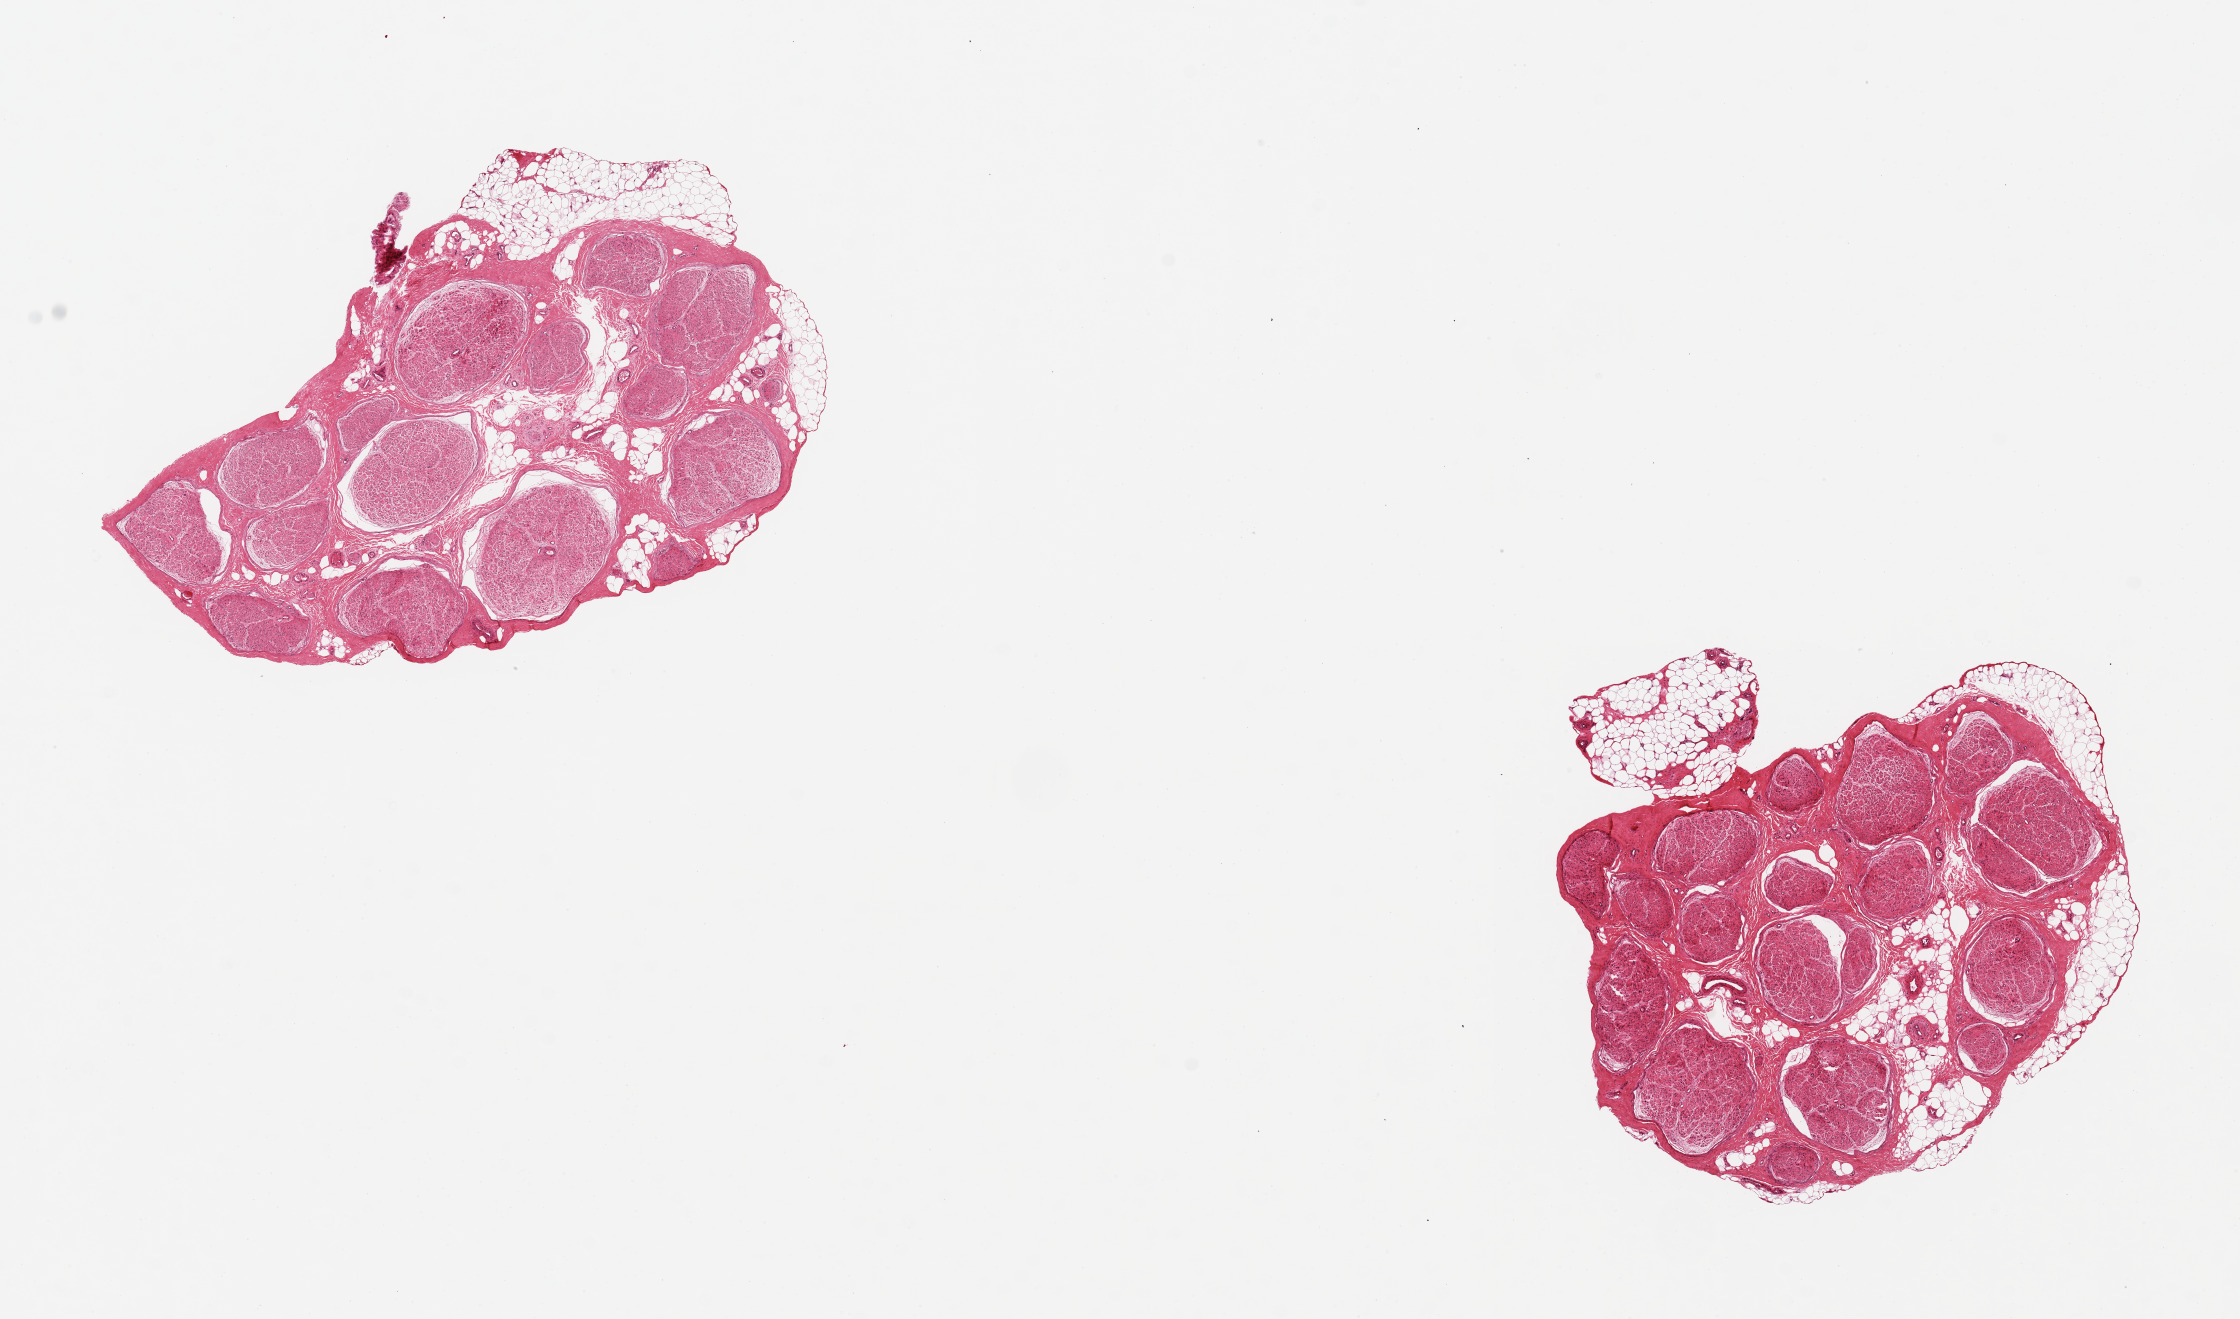
H&E whole-slide image, shown as a low-resolution overview of the whole scanned area (about 17.7 x 10.4 mm), PAXgene-fixed, paraffin-embedded tissue, target tissue: tibial nerve, tissue donor sample. Donor sex: male.
Reviewer comment on this tissue sample: 2 pieces ~5mm d. Minimal (`0.5mm) discontinuous foci of adherent fat, reasonably clean specimens.